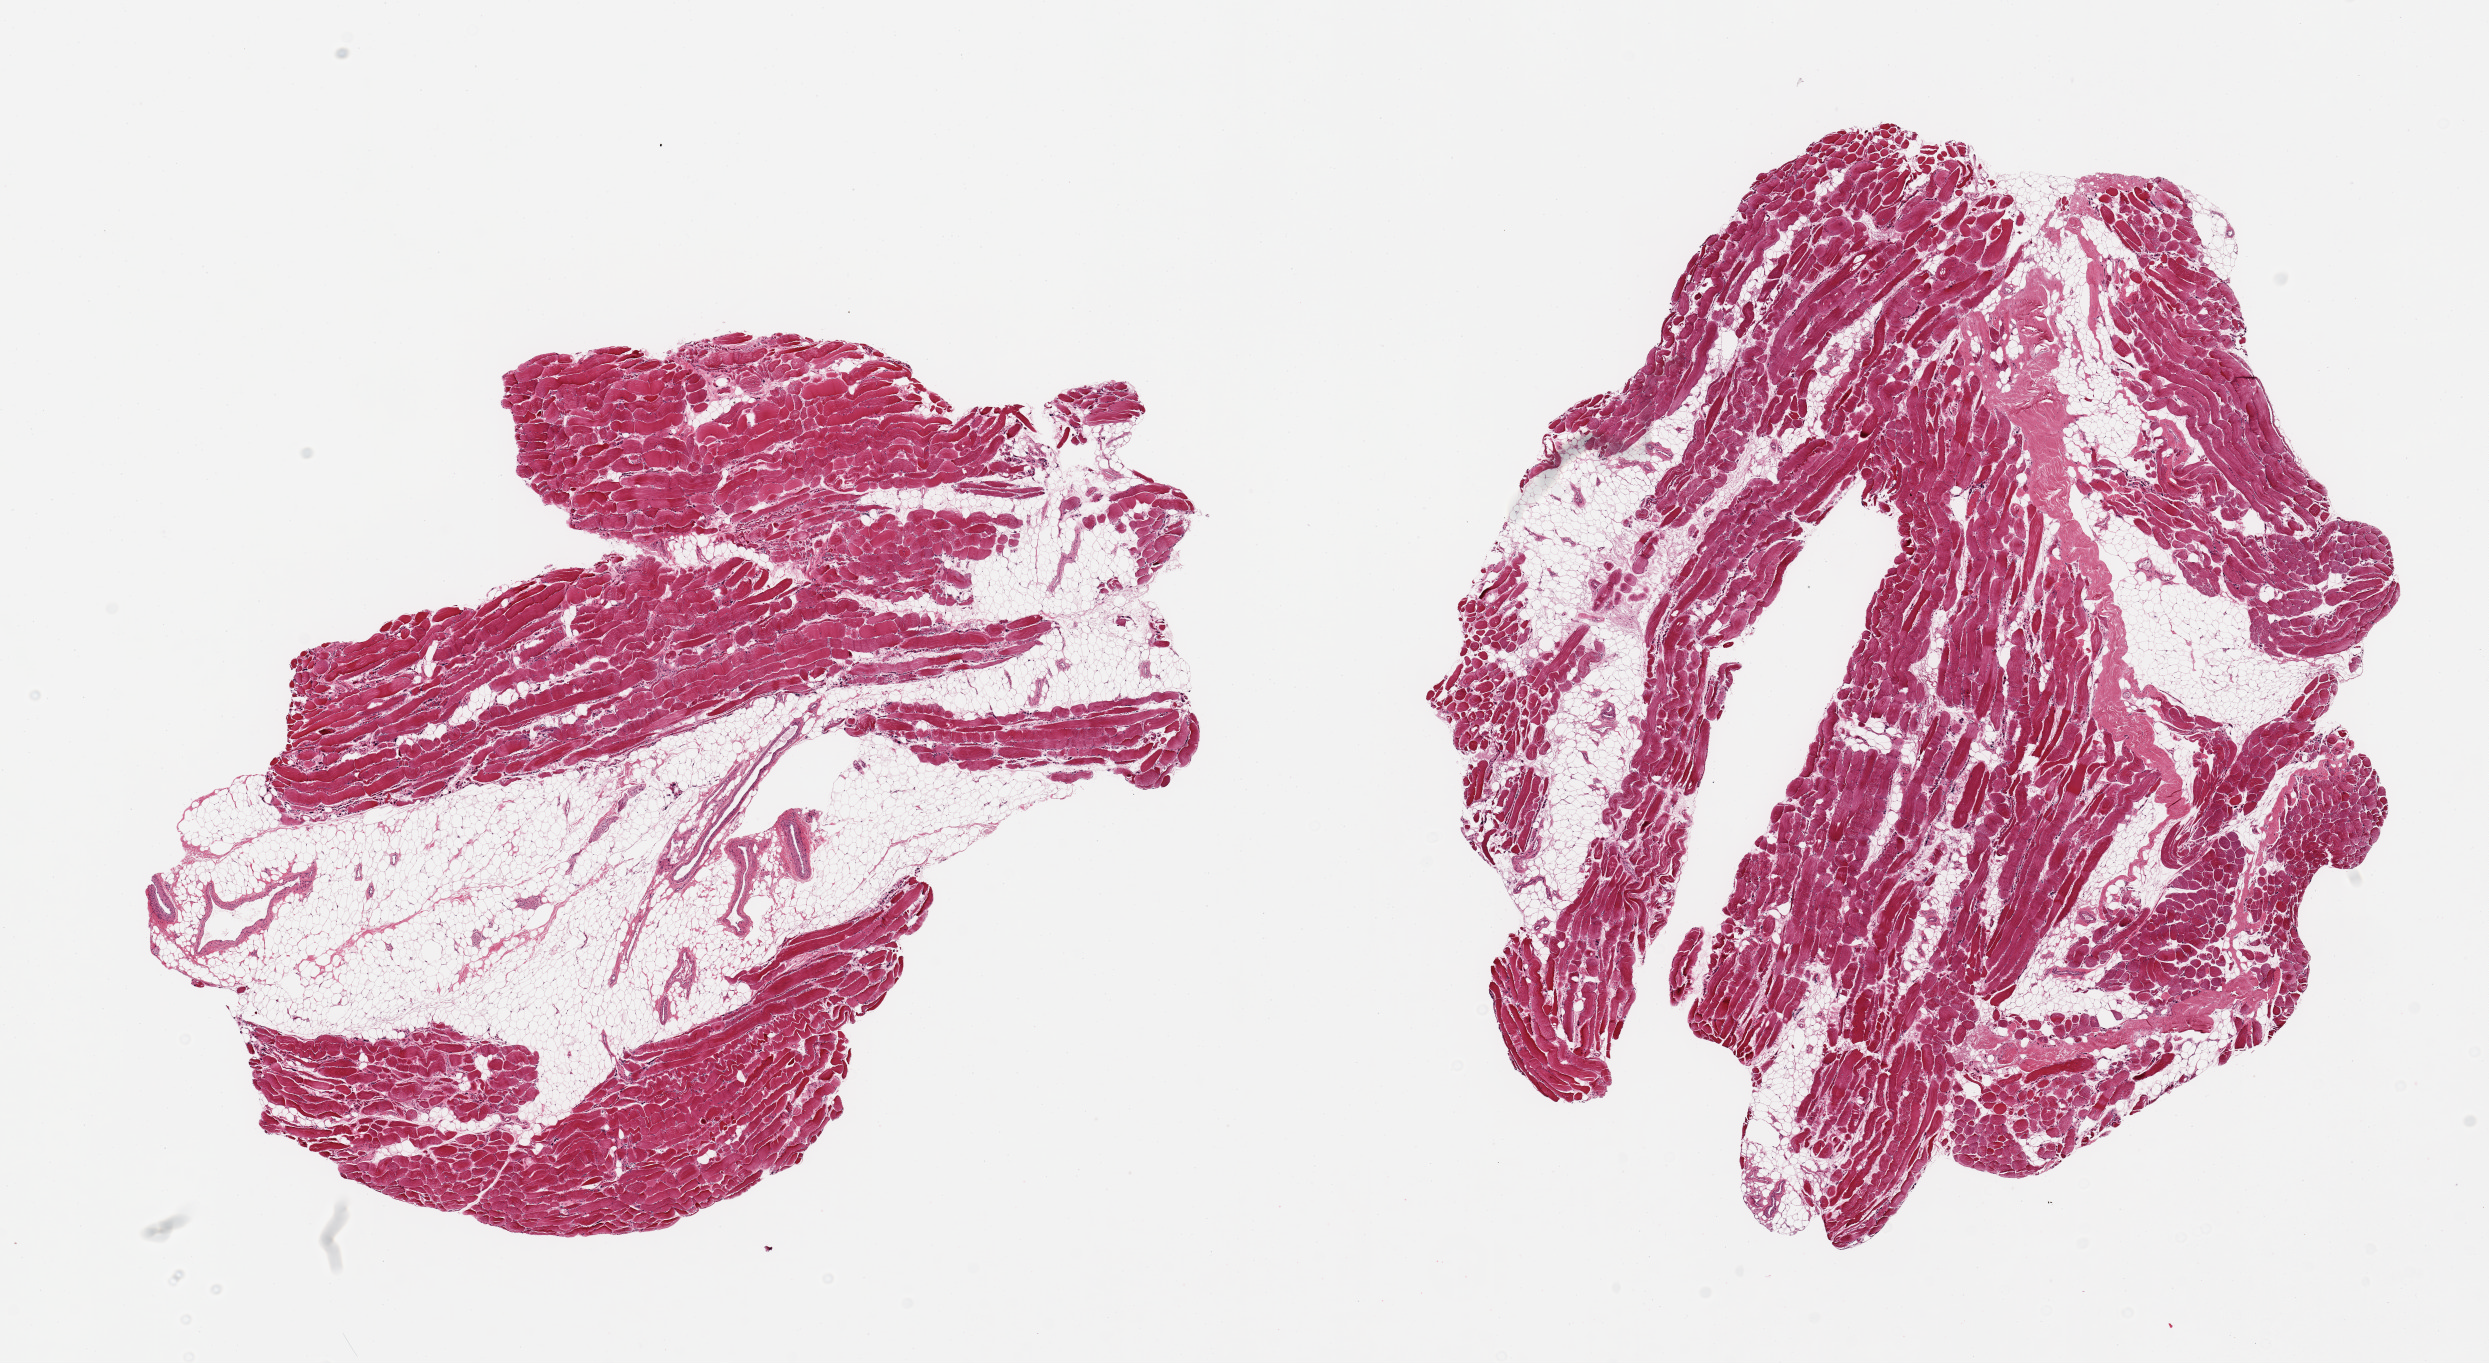
Digitized hematoxylin and eosin (H&E)-stained section, brightfield — low-resolution overview of the scanned area, about 19.7 x 10.8 mm, PAXgene-fixed, paraffin-embedded tissue, section of skeletal muscle (target tissue), tissue donor sample. Donor sex: female.
Reviewer comment on this tissue sample: 2 pieces; ~40% internal fat, some atrophy.